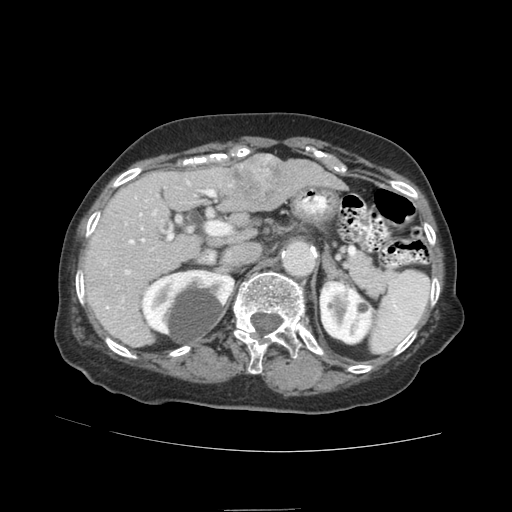
Contrast-enhanced abdominal CT (liver protocol), one axial slice. Position 53 of 89 along the scan axis. Soft-tissue window (W 400 / L 40 HU). 512 × 512 image matrix. From the clinical record (not read from this slice): diagnosis: hepatocellular carcinoma (patient treated with transarterial chemoembolisation; whether this scan precedes or follows treatment is not stated here); TNM stage (as recorded): Stage-II; Child-Pugh class: A; tumour nodularity: multinodular; tumour size: 4 cm.
Annotated regions visible in this slice (semi-automatic segmentation, software-assisted and operator-edited):
- liver parenchyma outside the tumour (the mass and vessels are separate outlines, so this box may not span the whole liver): bounding box [x1, y1, x2, y2] px = [84, 154, 335, 346]
- mass: [231, 154, 291, 211]
- liver vessels: [90, 179, 232, 329]